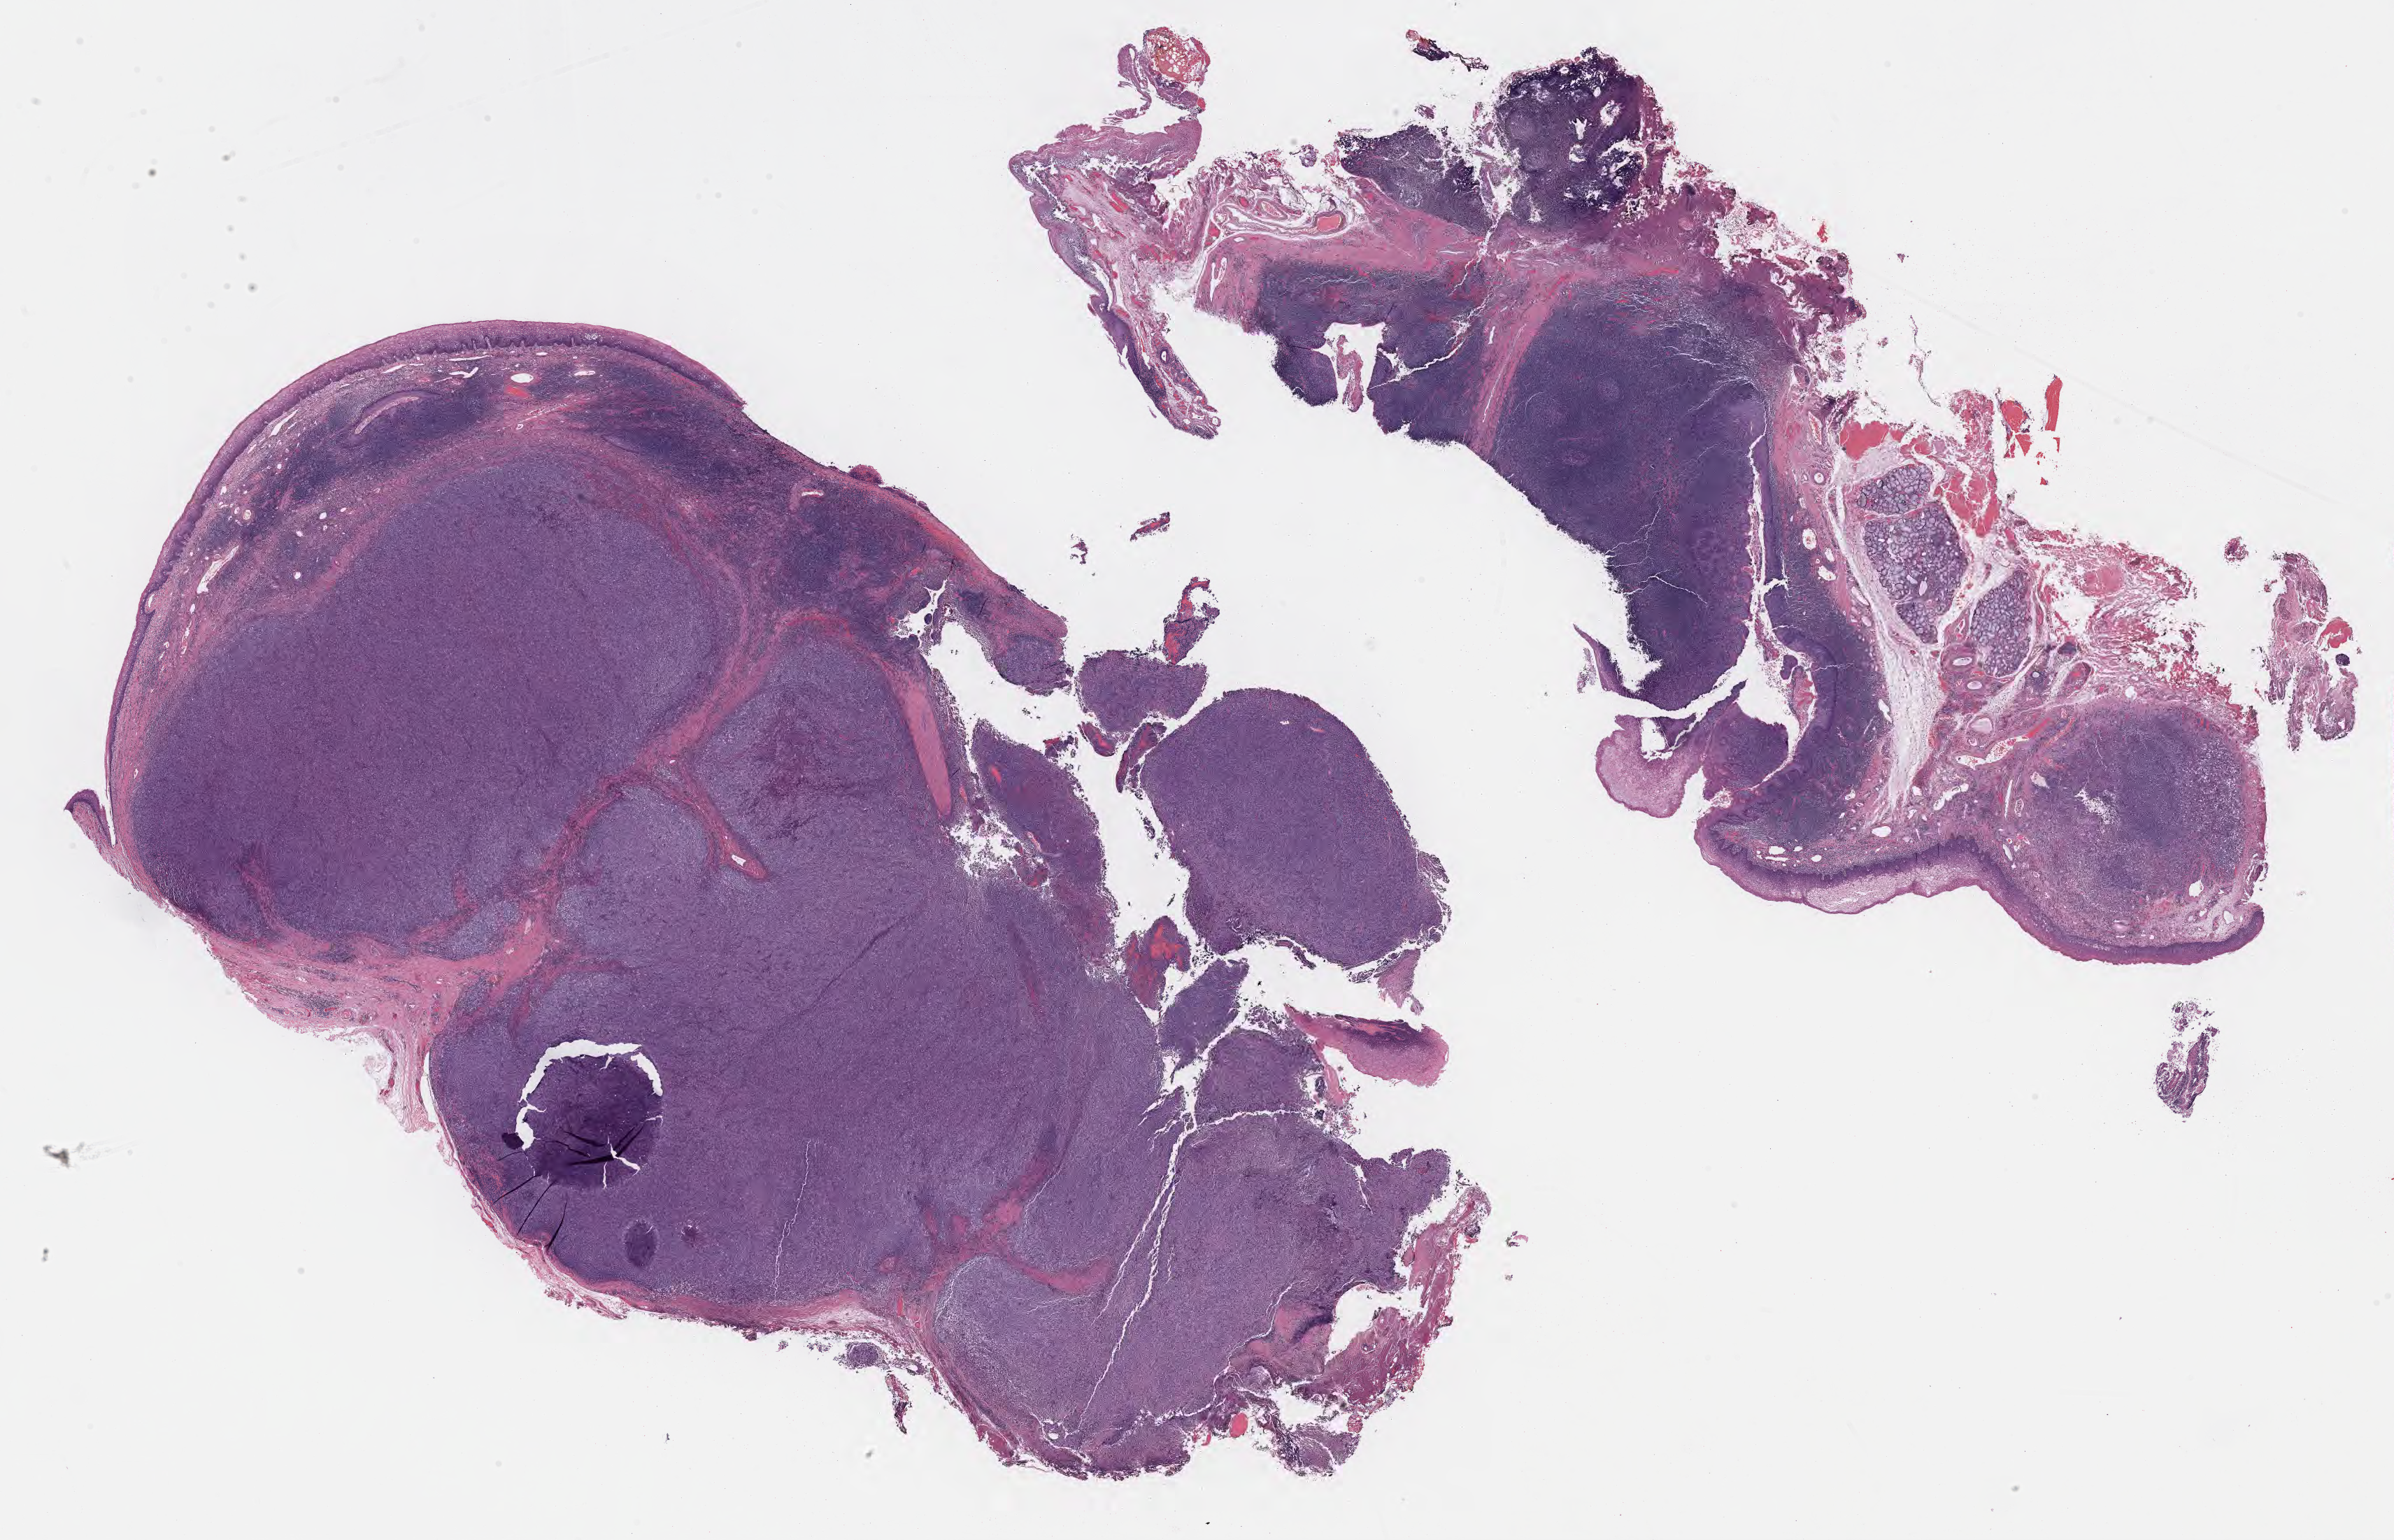
Whole-slide image, H&E stain, whole scanned area (about 27.7 x 17.8 mm) shown as a low-resolution overview, specimen: tumor tissue, anatomic site: lymph node. Patient: male, age 56 years.
Histologic diagnosis: Diffuse large B-cell lymphoma, NOS.